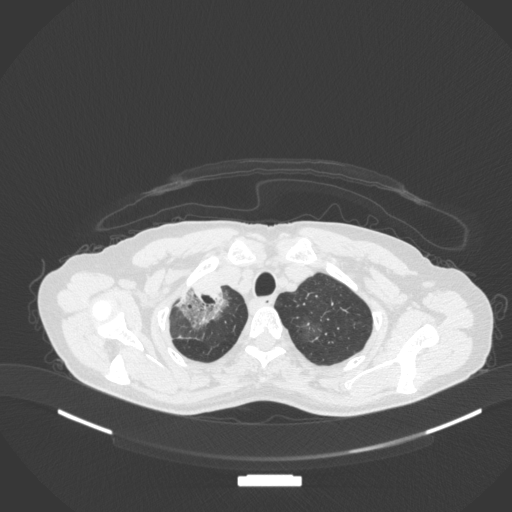
Chest CT, one axial slice. Position 284 of 311 along the scan axis. Reconstruction kernel B31f. 120 kVp. Lung window (W 1500 / L -600 HU). 512 × 512 image matrix. Female patient, age 59 years. From the clinical record (not read from this slice): clinical TNM (as recorded): T3 N0 M0; histopathological grade: G1.
Structures marked on this image (rectangle marked by the reading radiologist):
- lung tumour (recorded histology: adenocarcinoma): bounding box [x1, y1, x2, y2] px = [175, 276, 231, 332]